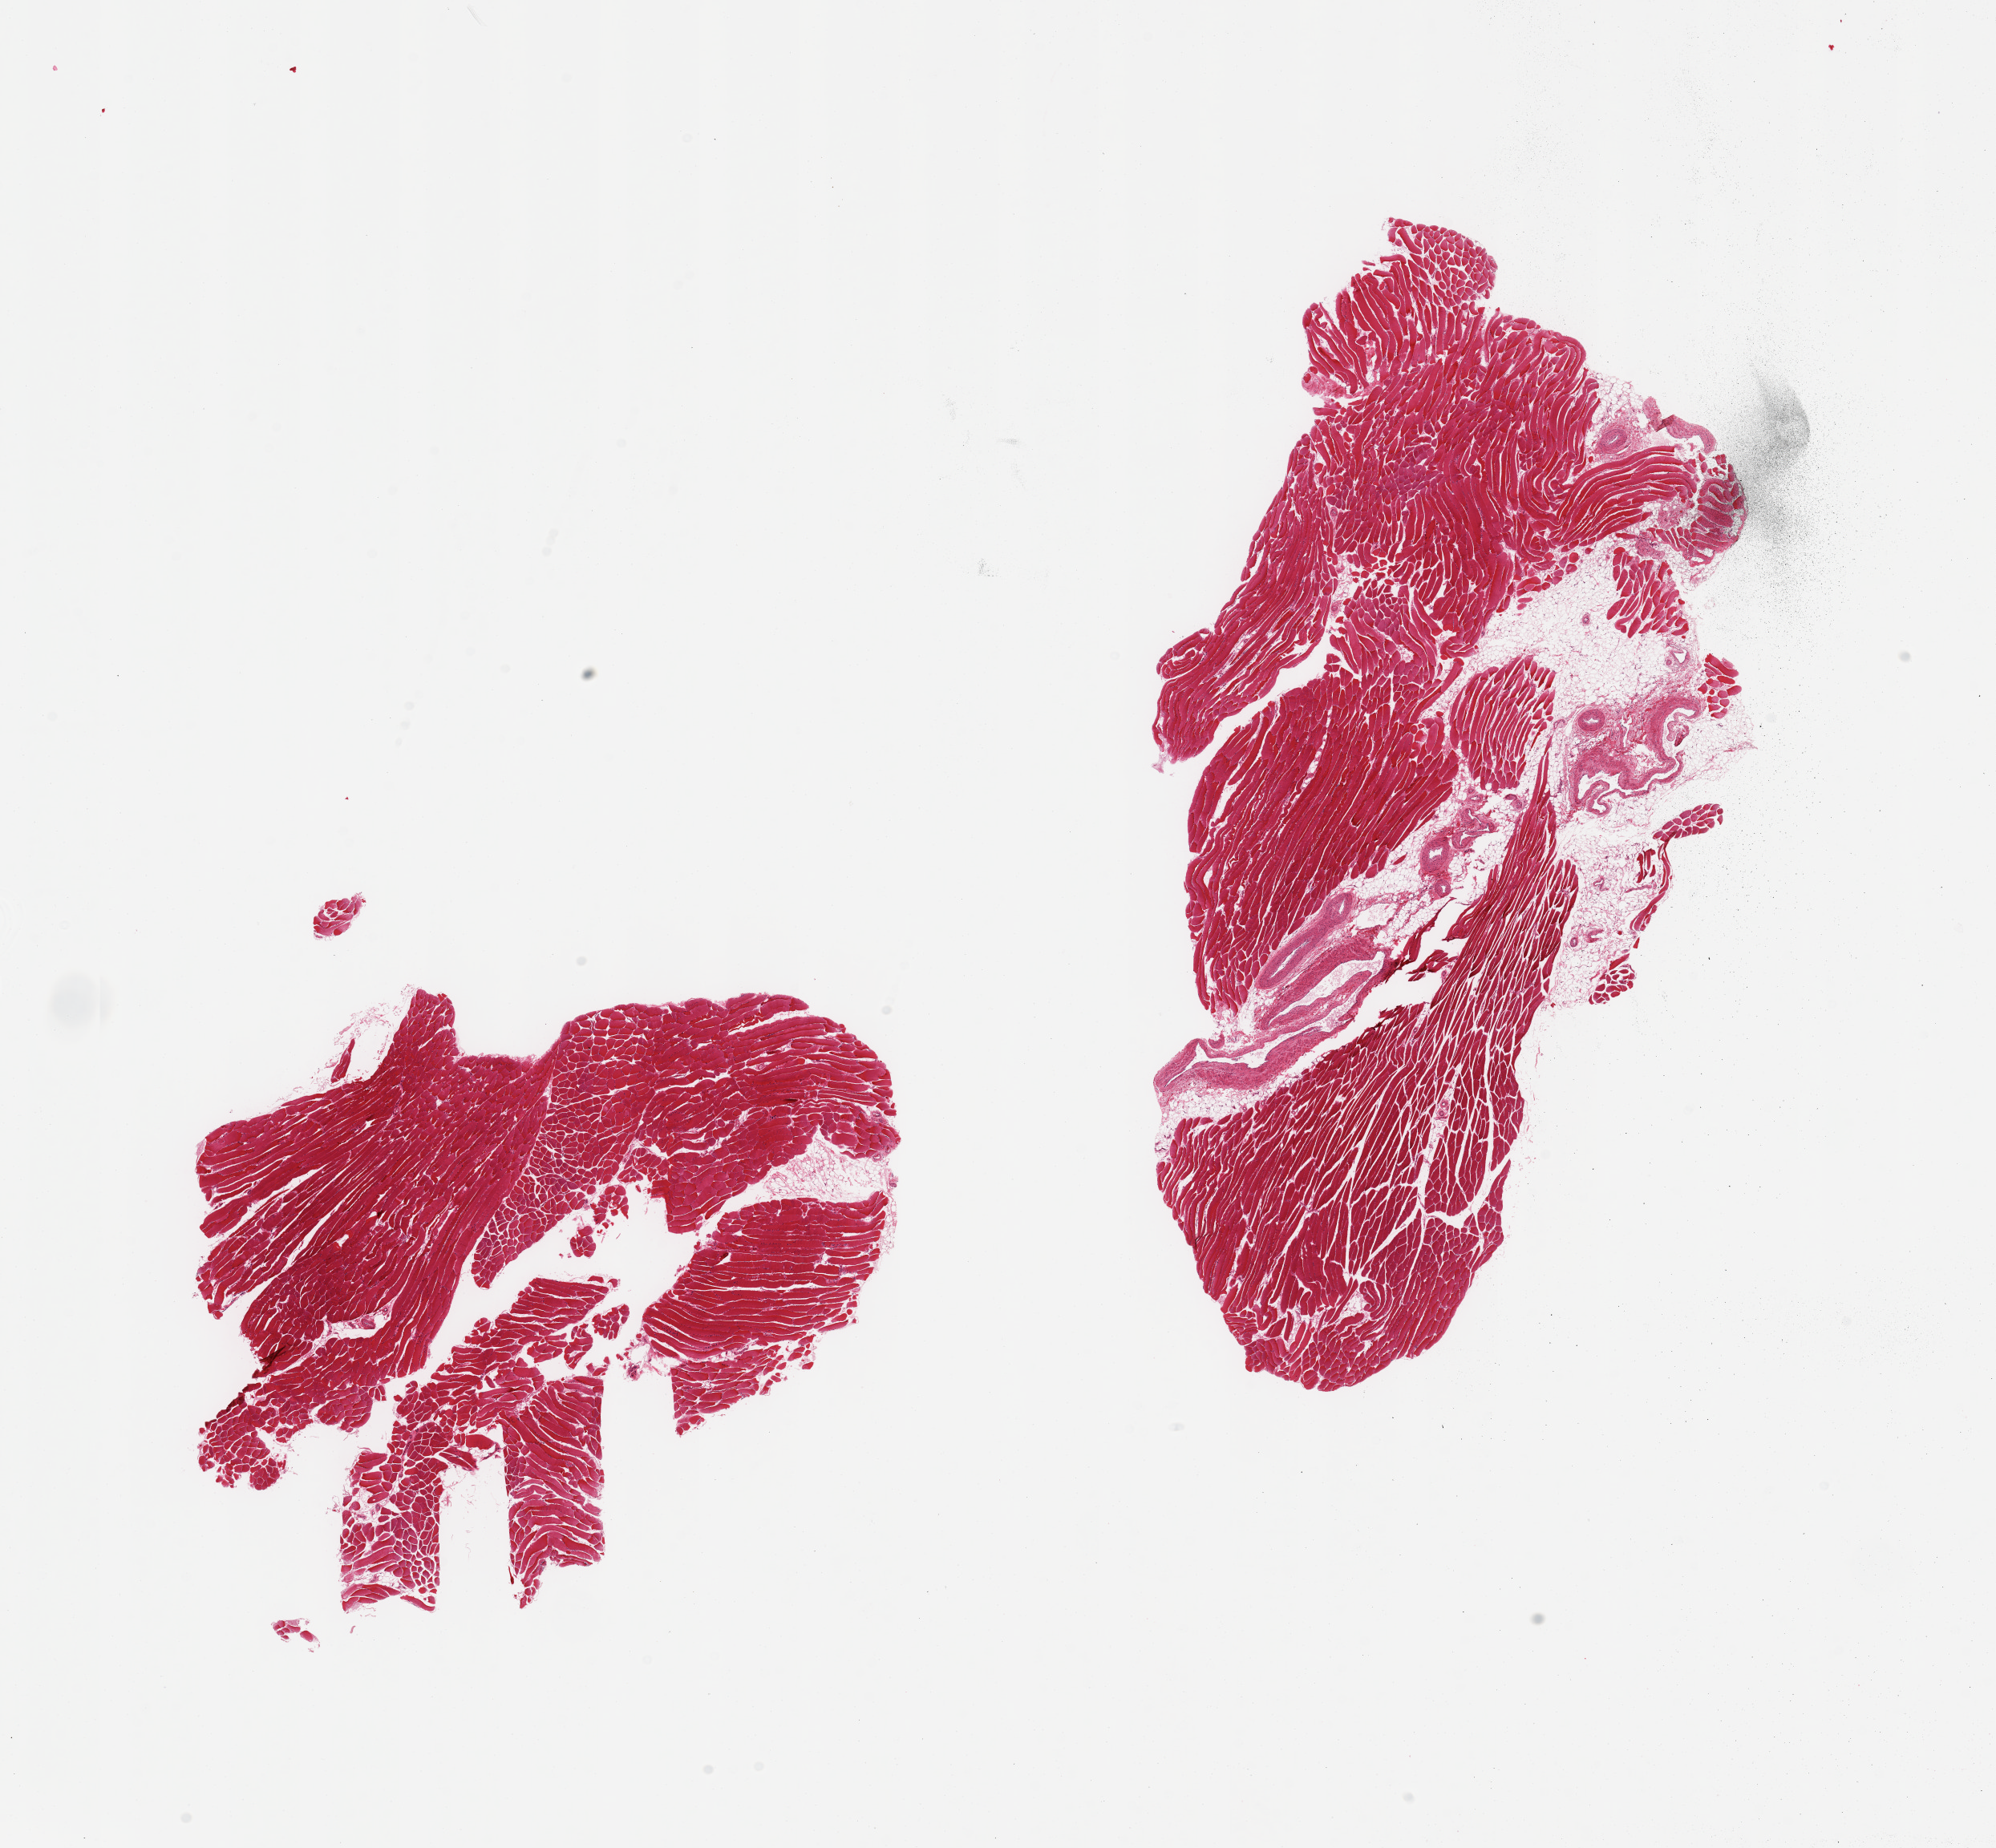
Whole-slide image, H&E stain — shown as a low-resolution overview of the whole scanned area (about 19.7 x 18.2 mm). PAXgene-fixed paraffin-embedded (PFPE) section. Target tissue: skeletal muscle. Donor tissue sample. Male donor.
Pathologist's review note for this sample: 2 pieces; ~10% interstitial fat/vascular elements.